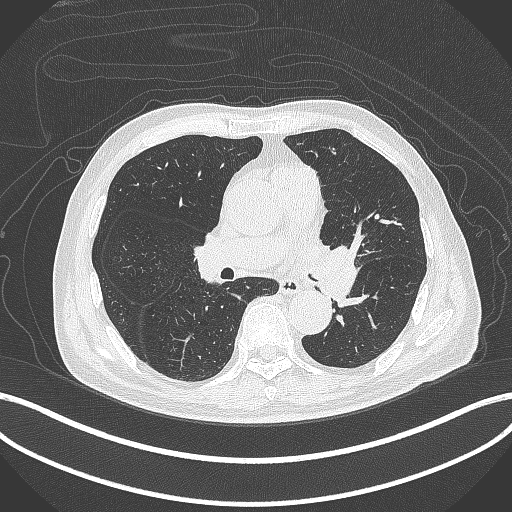
Chest CT, one axial slice; position 233 of 417 along the scan axis; 120 kVp; lung window (W 1500 / L -600 HU); 1 mm slice thickness; 512 × 512 image matrix, field of view 400 × 400 mm. Patient: male, 77 years. Case-level facts recorded for this patient, not image findings: clinical TNM (as recorded): T3 N1 M0.
Annotated regions visible in this slice (rectangle marked by the reading radiologist):
- lung tumour (recorded histology: adenocarcinoma): box from (x=314, y=243) to (x=366, y=307) px